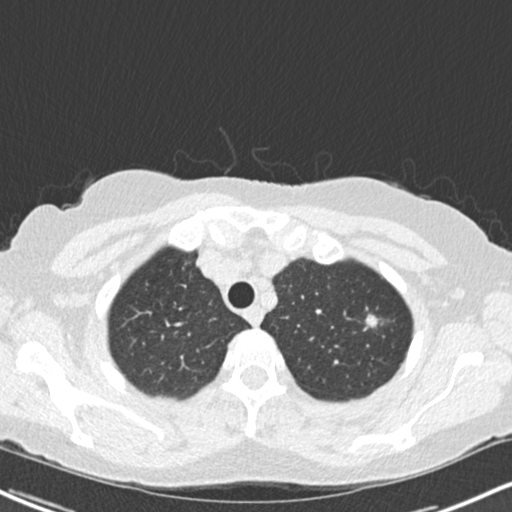
Axial slice from a low-dose chest CT screening exam; first (baseline) screen; lung window (W 1500 / L -600 HU); 2 mm slice thickness; 512 × 512 image matrix, field of view 319 × 319 mm. Female, age 64 years at enrolment. Former smoker at enrolment.
Lesion marked by an expert reader, bounding box (x1, y1, x2, y2) in pixels: (358, 307, 389, 338). The screening reader recorded 2 non-calcified nodules or masses ≥4 mm on this exam; which of them this box marks is not recorded. Participant outcome: lung cancer diagnosed 477 days after this screen (after the second annual screen) — signet ring cell carcinoma, right upper lobe, poorly differentiated (G3), stage IA (AJCC 6th edition), 15 mm at pathology.